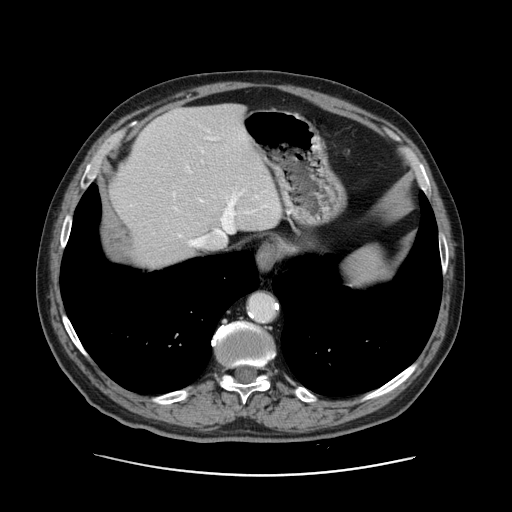
Contrast-enhanced abdominal CT, one axial slice. Slice 108 of 141 in the series (ordered by position). 120 kVp. Intravenous contrast given. Soft-tissue window (W 400 / L 40 HU). 2.5 mm slice thickness. 512 × 512 image matrix, field of view 395 × 395 mm. Male patient, age 72 years. Case-level facts recorded for this patient, not image findings: diagnosis: colorectal cancer liver metastases, imaged before liver resection; multiple liver metastases: yes; largest metastasis: 5.4 cm; disease in both lobes: yes.
Outlined on this slice (manually delineated by an expert):
- hepatic veins: box from (x=173, y=130) to (x=270, y=247) px
- liver: (x=111, y=103)–(x=282, y=270)
- planned liver remnant (the part of the liver to remain after resection): (x=142, y=104)–(x=282, y=270)
- portal vein (with intrahepatic branches): (x=191, y=137)–(x=245, y=241)